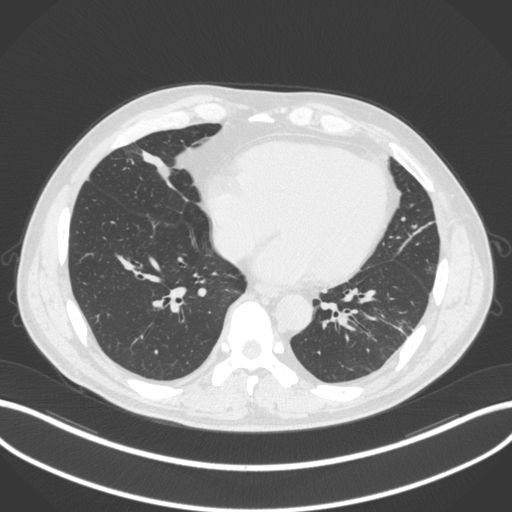
Chest CT, one axial slice; position 89 of 399 along the scan axis; reconstruction kernel B31f; lung window (W 1500 / L -600 HU); 1 mm slice thickness; 512 × 512 image matrix. Male patient, age 59 years. From the clinical record (not read from this slice): clinical TNM (as recorded): T2a N1 M0.
Annotated regions visible in this slice (rectangle marked by the reading radiologist):
- lung tumour (recorded histology: adenocarcinoma): box from (x=135, y=141) to (x=175, y=184) px